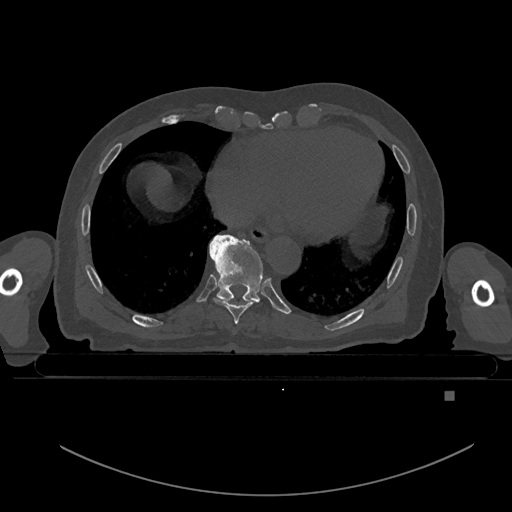
CT including the spine, one axial slice; slice 173 of 969 in the series (ordered by position); bone window (W 1800 / L 400 HU); 512 × 512 image matrix, field of view 456 × 456 mm. Patient: male, 82 years. From the clinical record (not read from this slice): primary cancer: prostate.
Structures marked on this image (semi-automatically segmented with operator editing):
- T8 vertebra: bounding box (x1, y1, x2, y2) in pixels: (213, 297, 254, 324)
- T9 vertebra: (209, 234, 263, 303)